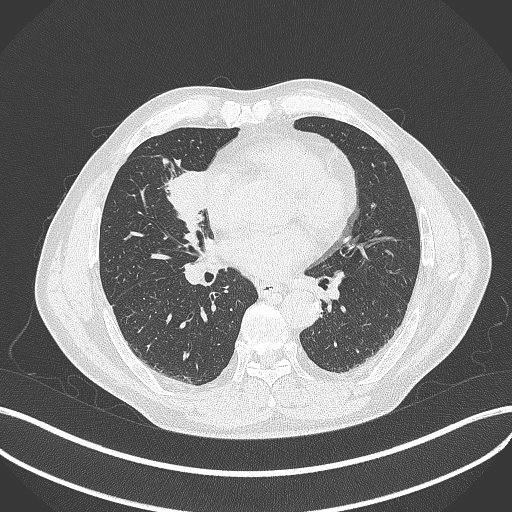
Chest CT, one axial slice. Slice 188 of 429 in the series (ordered by position). Reconstruction kernel B70f. 120 kVp. Lung window (W 1500 / L -600 HU). 1 mm slice thickness. 512 × 512 image matrix, field of view 400 × 400 mm. Male patient, age 61 years. Case-level facts recorded for this patient, not image findings: clinical TNM (as recorded): T2b N1 M0.
Structures marked on this image (bounding box drawn by a radiologist):
- lung tumour (recorded histology: squamous cell carcinoma): bounding box [x1, y1, x2, y2] px = [162, 157, 215, 231]